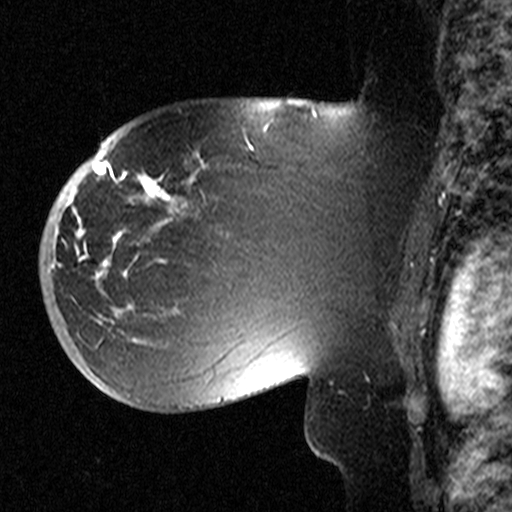
Breast MRI (dynamic contrast-enhanced), one sagittal slice. Position 30 of 44 along the scan axis. Dynamic contrast-enhanced study with each time point stored as its own series, time point 2 of 3 at this slice position (early post-contrast, ordered by acquisition time). 1.5 T. TE 4.5 ms, TR 11 ms. 3.27 mm slice thickness. 512 × 512 image matrix, field of view 200 × 200 mm. Patient: female, 53 years. From the clinical record (not read from this slice): setting: breast cancer imaged before/during neoadjuvant chemotherapy; receptor status: HR-positive, HER2-negative.
Annotated regions visible in this slice (semi-automatically segmented with operator editing):
- analysis volume of interest (the breast-tissue region the enhancement analysis was run in; not a lesion): box from (x=58, y=154) to (x=311, y=367) px
- tumour enhancement mask (voxels above the 90 % enhancement threshold inside the analysis volume of interest): (x=74, y=159)–(x=203, y=272)